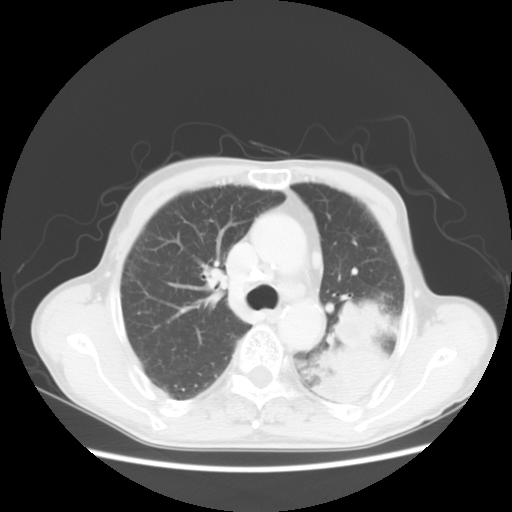
Chest CT, one axial slice; position 36 of 51 along the scan axis; lung window (W 1500 / L -600 HU); 512 × 512 image matrix. Patient: male, 64 years. From the clinical record (not read from this slice): clinical TNM (as recorded): T4 N0 M0.
Outlined on this slice (rectangle marked by the reading radiologist):
- lung tumour (recorded histology: squamous cell carcinoma): bounding box [x1, y1, x2, y2] px = [311, 304, 401, 409]